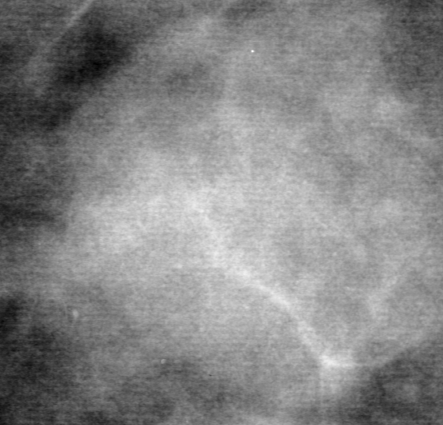
Cropped region of a digitized screen-film mammogram centred on a radiologist-marked abnormality, left breast, CC view.
Finding: mass, shape oval, margins obscured; BI-RADS assessment category 3; subtlety rating 2 on a 1 (subtle) to 5 (obvious) scale; pathology result (as recorded, not read from the image): benign.